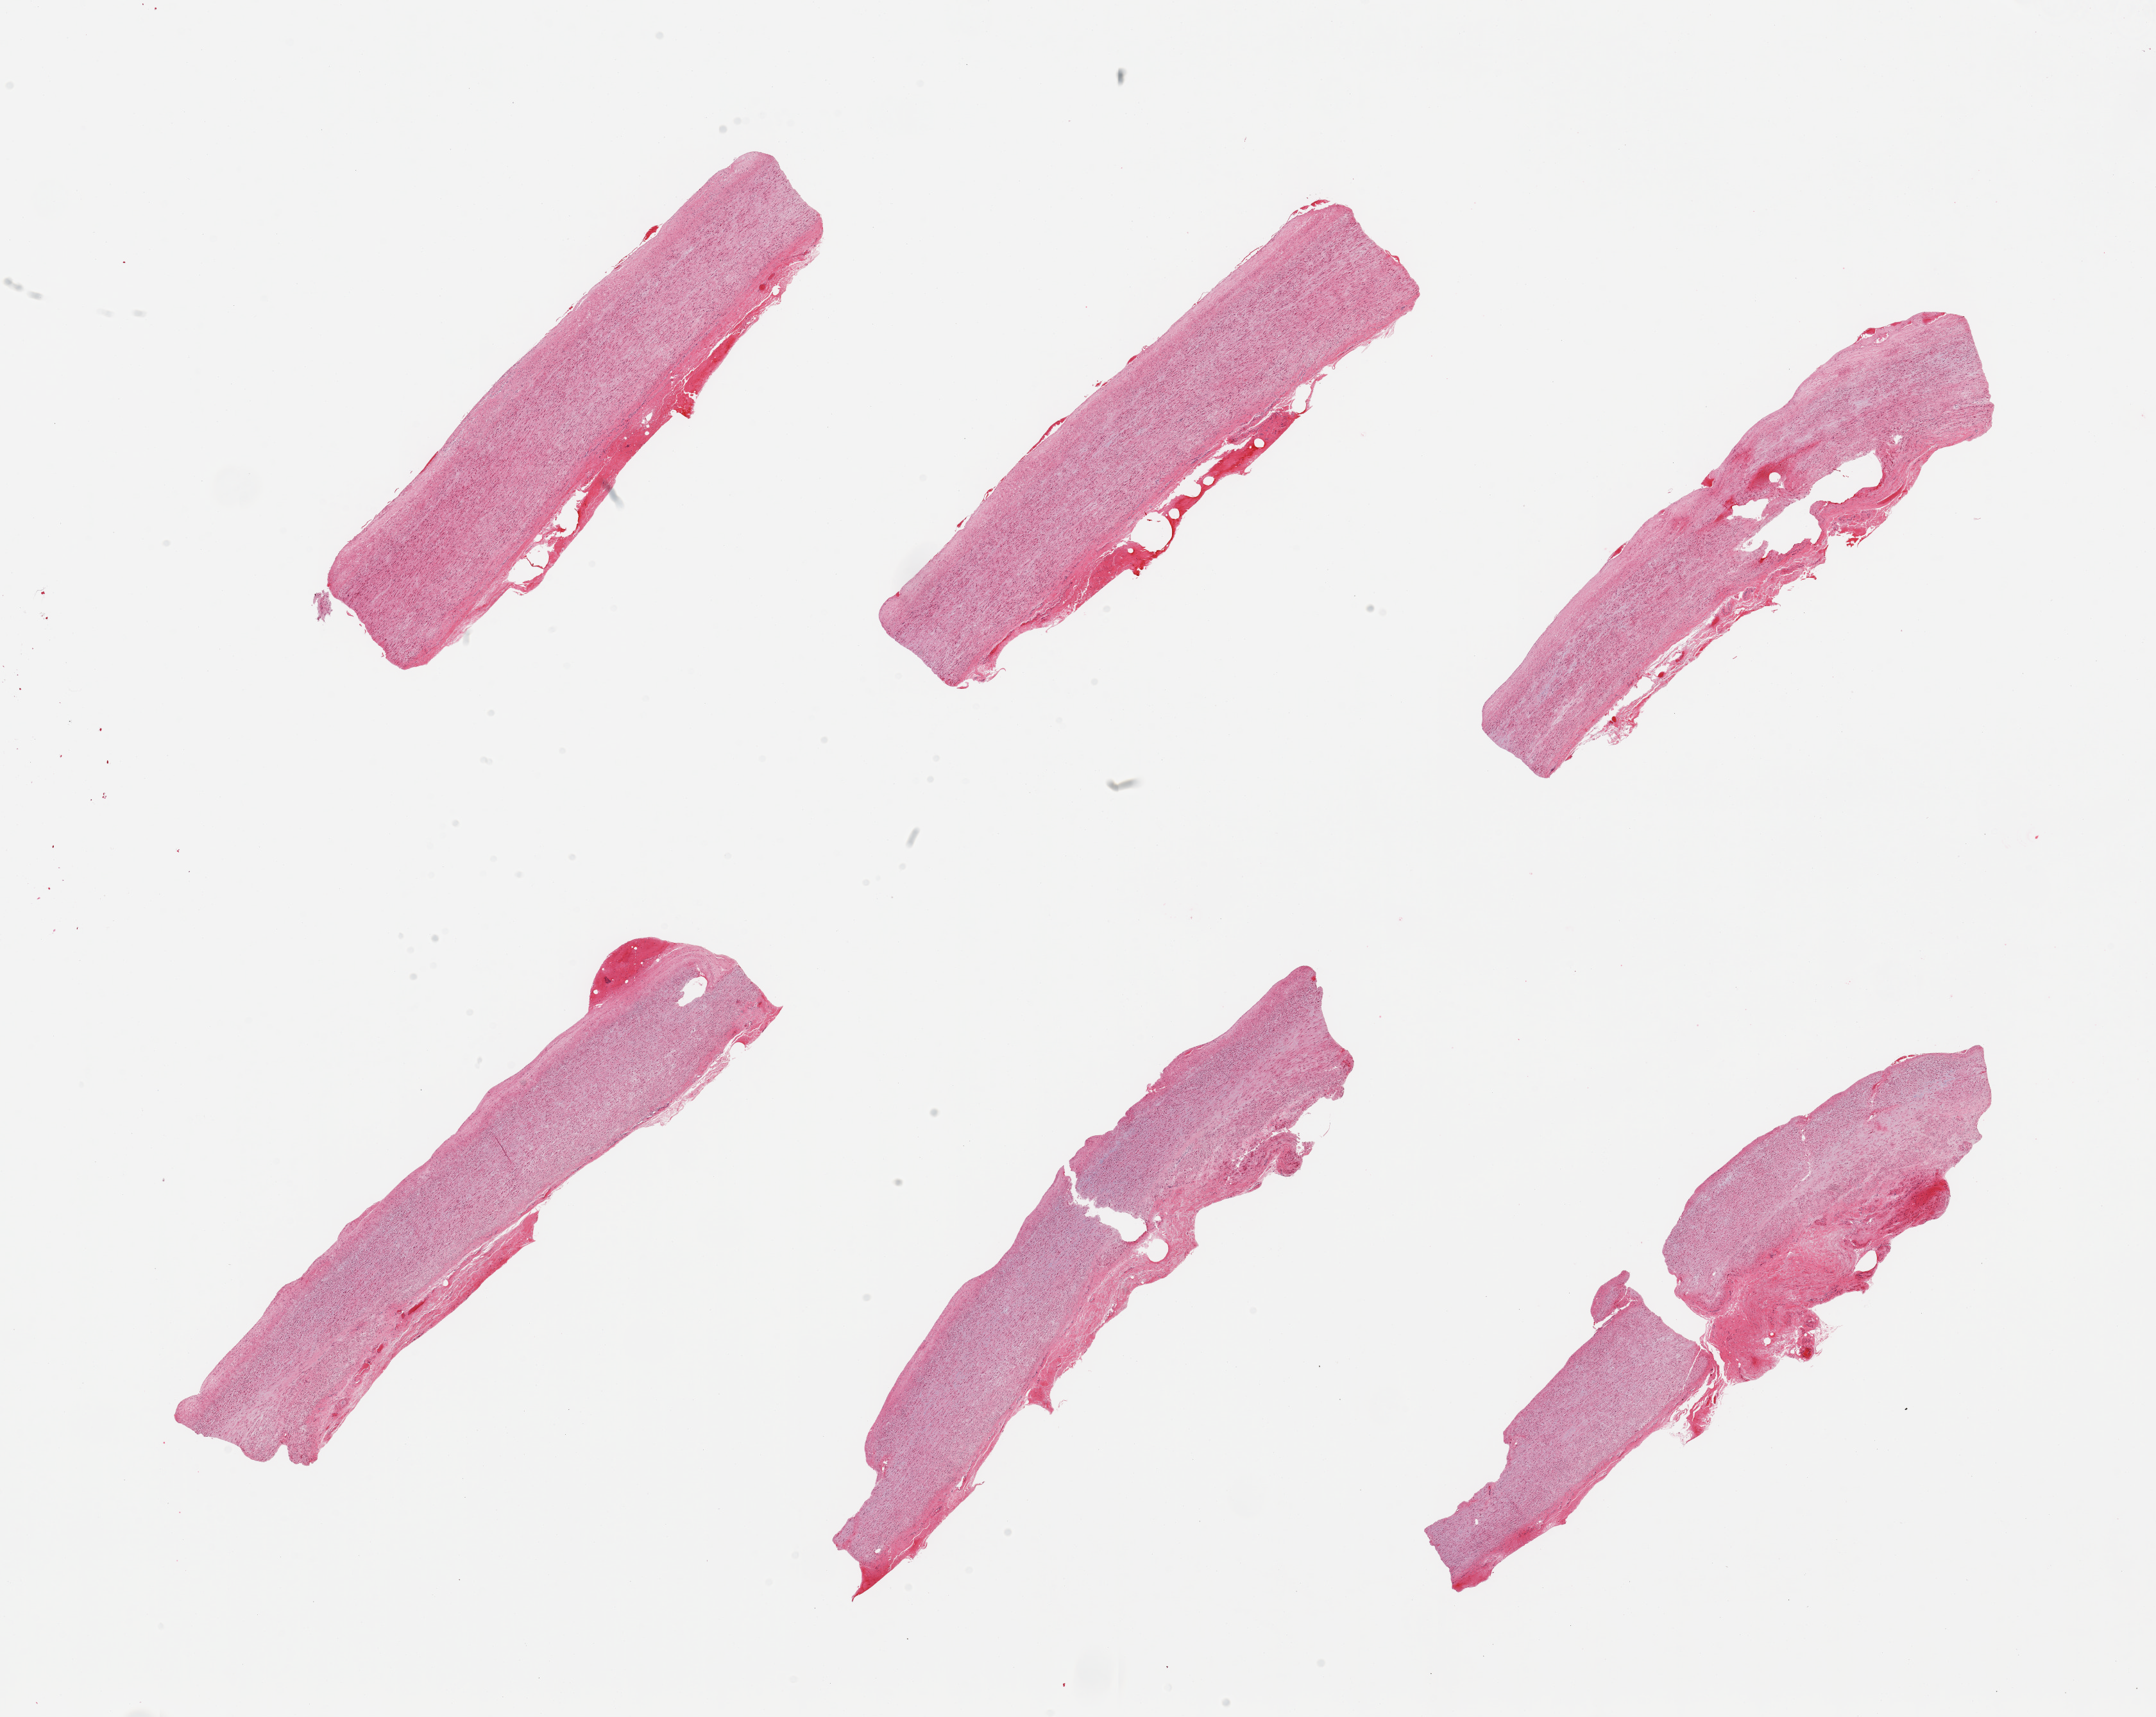
Whole-slide image, H&E stain — whole scanned area (about 26.6 x 21.2 mm, acquisition: 20x scan) shown as a low-resolution overview; PAXgene-fixed paraffin-embedded (PFPE) section; sampled site (target tissue): aorta; donor tissue sample.
Review note (as recorded): 6 pieces; moderate flat plaques.